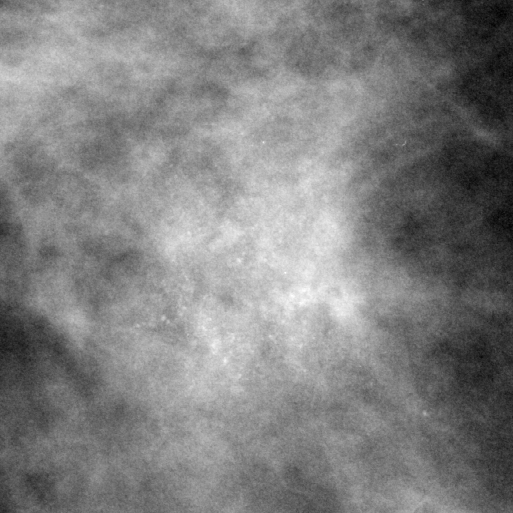
Region of interest cut from a scanned film mammogram (one marked finding), right breast, CC view.
- Finding: calcifications, morphology amorphous, distribution clustered; BI-RADS assessment category 4; subtlety rating 3 on a 1 (subtle) to 5 (obvious) scale; pathology (as recorded): benign.